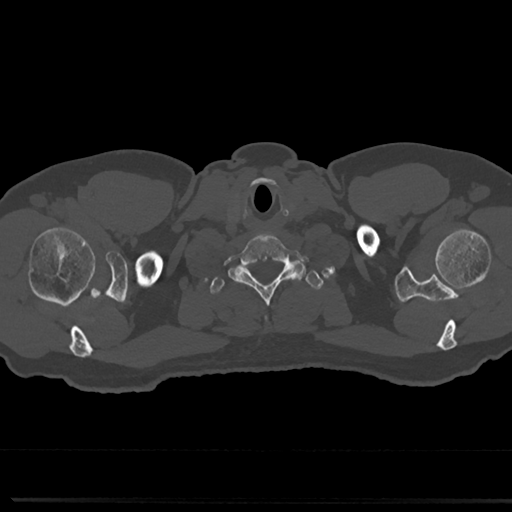
CT including the spine, one axial slice. Bone window (W 1800 / L 400 HU). 0.5 mm slice thickness. 512 × 512 image matrix, field of view 355 × 355 mm. Patient: male, 61 years. Case-level facts recorded for this patient, not image findings: primary cancer: prostate.
Annotated regions visible in this slice (semi-automatically segmented with operator editing):
- T1 vertebra: bounding box [x1, y1, x2, y2] px = [209, 265, 319, 295]